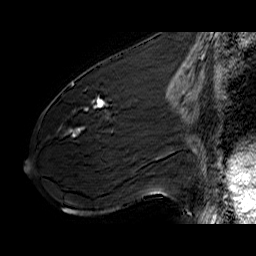
Breast MRI (dynamic contrast-enhanced), one sagittal slice. Slice 30 of 60 in the series (ordered by position). Dynamic contrast-enhanced series, time point 2 of 6 at this slice position (early post-contrast). 1.5 T. TE 6.4 ms, TR 32.9 ms. 256 × 256 image matrix, field of view 200 × 200 mm. Female patient. Case-level facts recorded for this patient, not image findings: setting: breast cancer imaged before/during neoadjuvant chemotherapy; receptor status: HER2-positive.
Structures marked on this image (semi-automatically segmented with operator editing):
- analysis volume of interest (the breast-tissue region the enhancement analysis was run in; not a lesion): bounding box (x1, y1, x2, y2) in pixels: (61, 77, 141, 142)
- tumour enhancement mask (voxels above the 100 % enhancement threshold inside the analysis volume of interest): (70, 96, 110, 132)